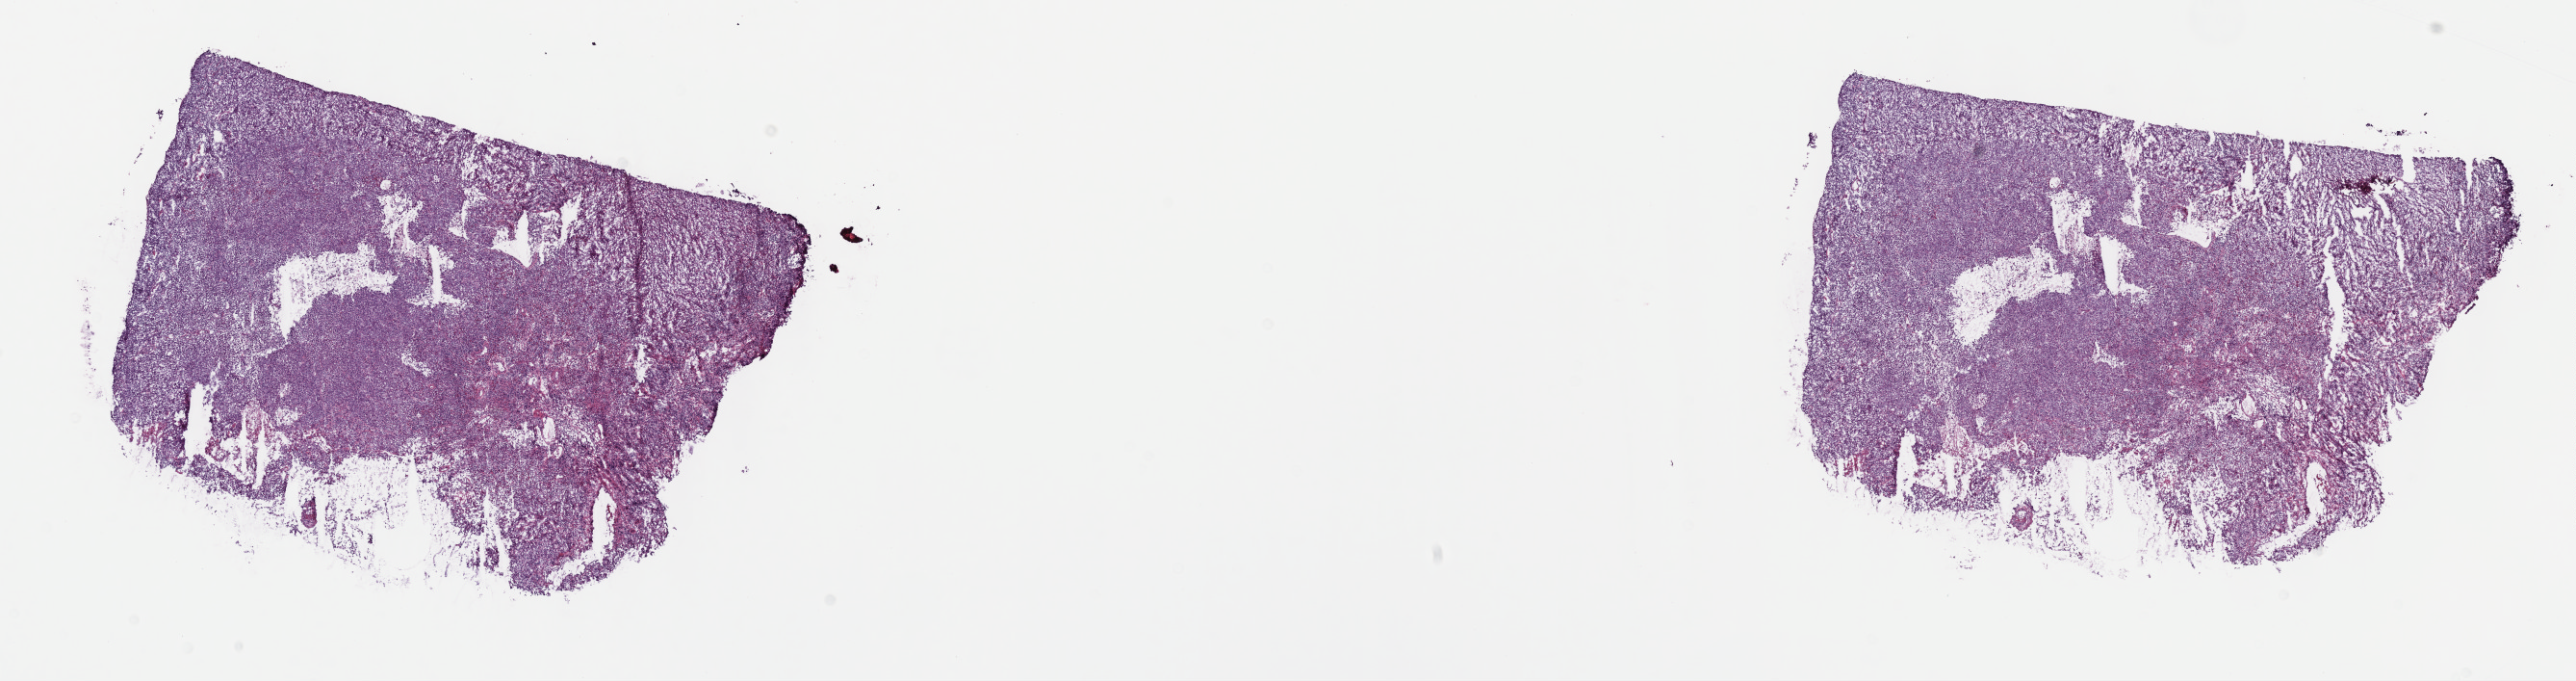
H&E whole-slide image — a low-resolution overview of the entire scanned area, about 21.6 x 5.7 mm (acquisition: 40x scan); frozen section; cervix, primary tumour sample. Female, age 54 years at initial diagnosis. Histologic grade: G3 (poorly differentiated). Slide review estimates, as recorded: tumour cells 70%, tumour nuclei 70%, normal cells 0%, stromal cells 10%, necrosis 20%. Infiltration values recorded for this section: lymphocyte infiltration 30%, monocyte infiltration 0%, neutrophil infiltration 70%.
FIGO stage: IIB. Lymph nodes positive (case pathology): 0 of 51 examined. Diagnosis: Squamous cell carcinoma, NOS (cervix uteri).